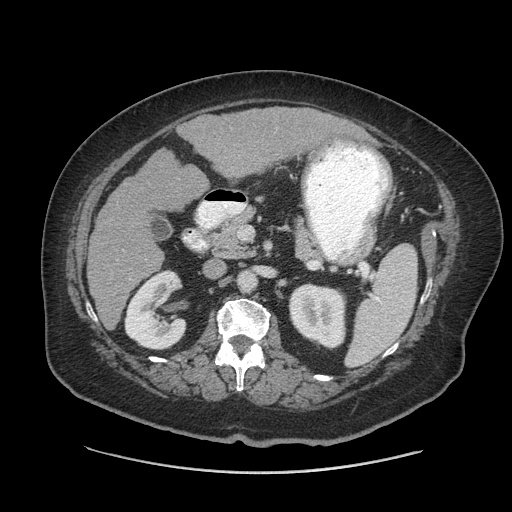
Contrast-enhanced abdominal CT (liver protocol), one axial slice; position 30 of 91 along the scan axis; 140 kVp; soft-tissue window (W 400 / L 40 HU); 2.5 mm slice thickness; 512 × 512 image matrix. Case-level facts recorded for this patient, not image findings: diagnosis: hepatocellular carcinoma (patient treated with transarterial chemoembolisation; whether this scan precedes or follows treatment is not stated here); TNM stage (as recorded): Stage-I; Child-Pugh class: A.
Structures marked on this image (semi-automatically segmented with operator editing):
- liver parenchyma outside the tumour (the mass and vessels are separate outlines, so this box may not span the whole liver): bounding box [x1, y1, x2, y2] px = [88, 106, 358, 328]